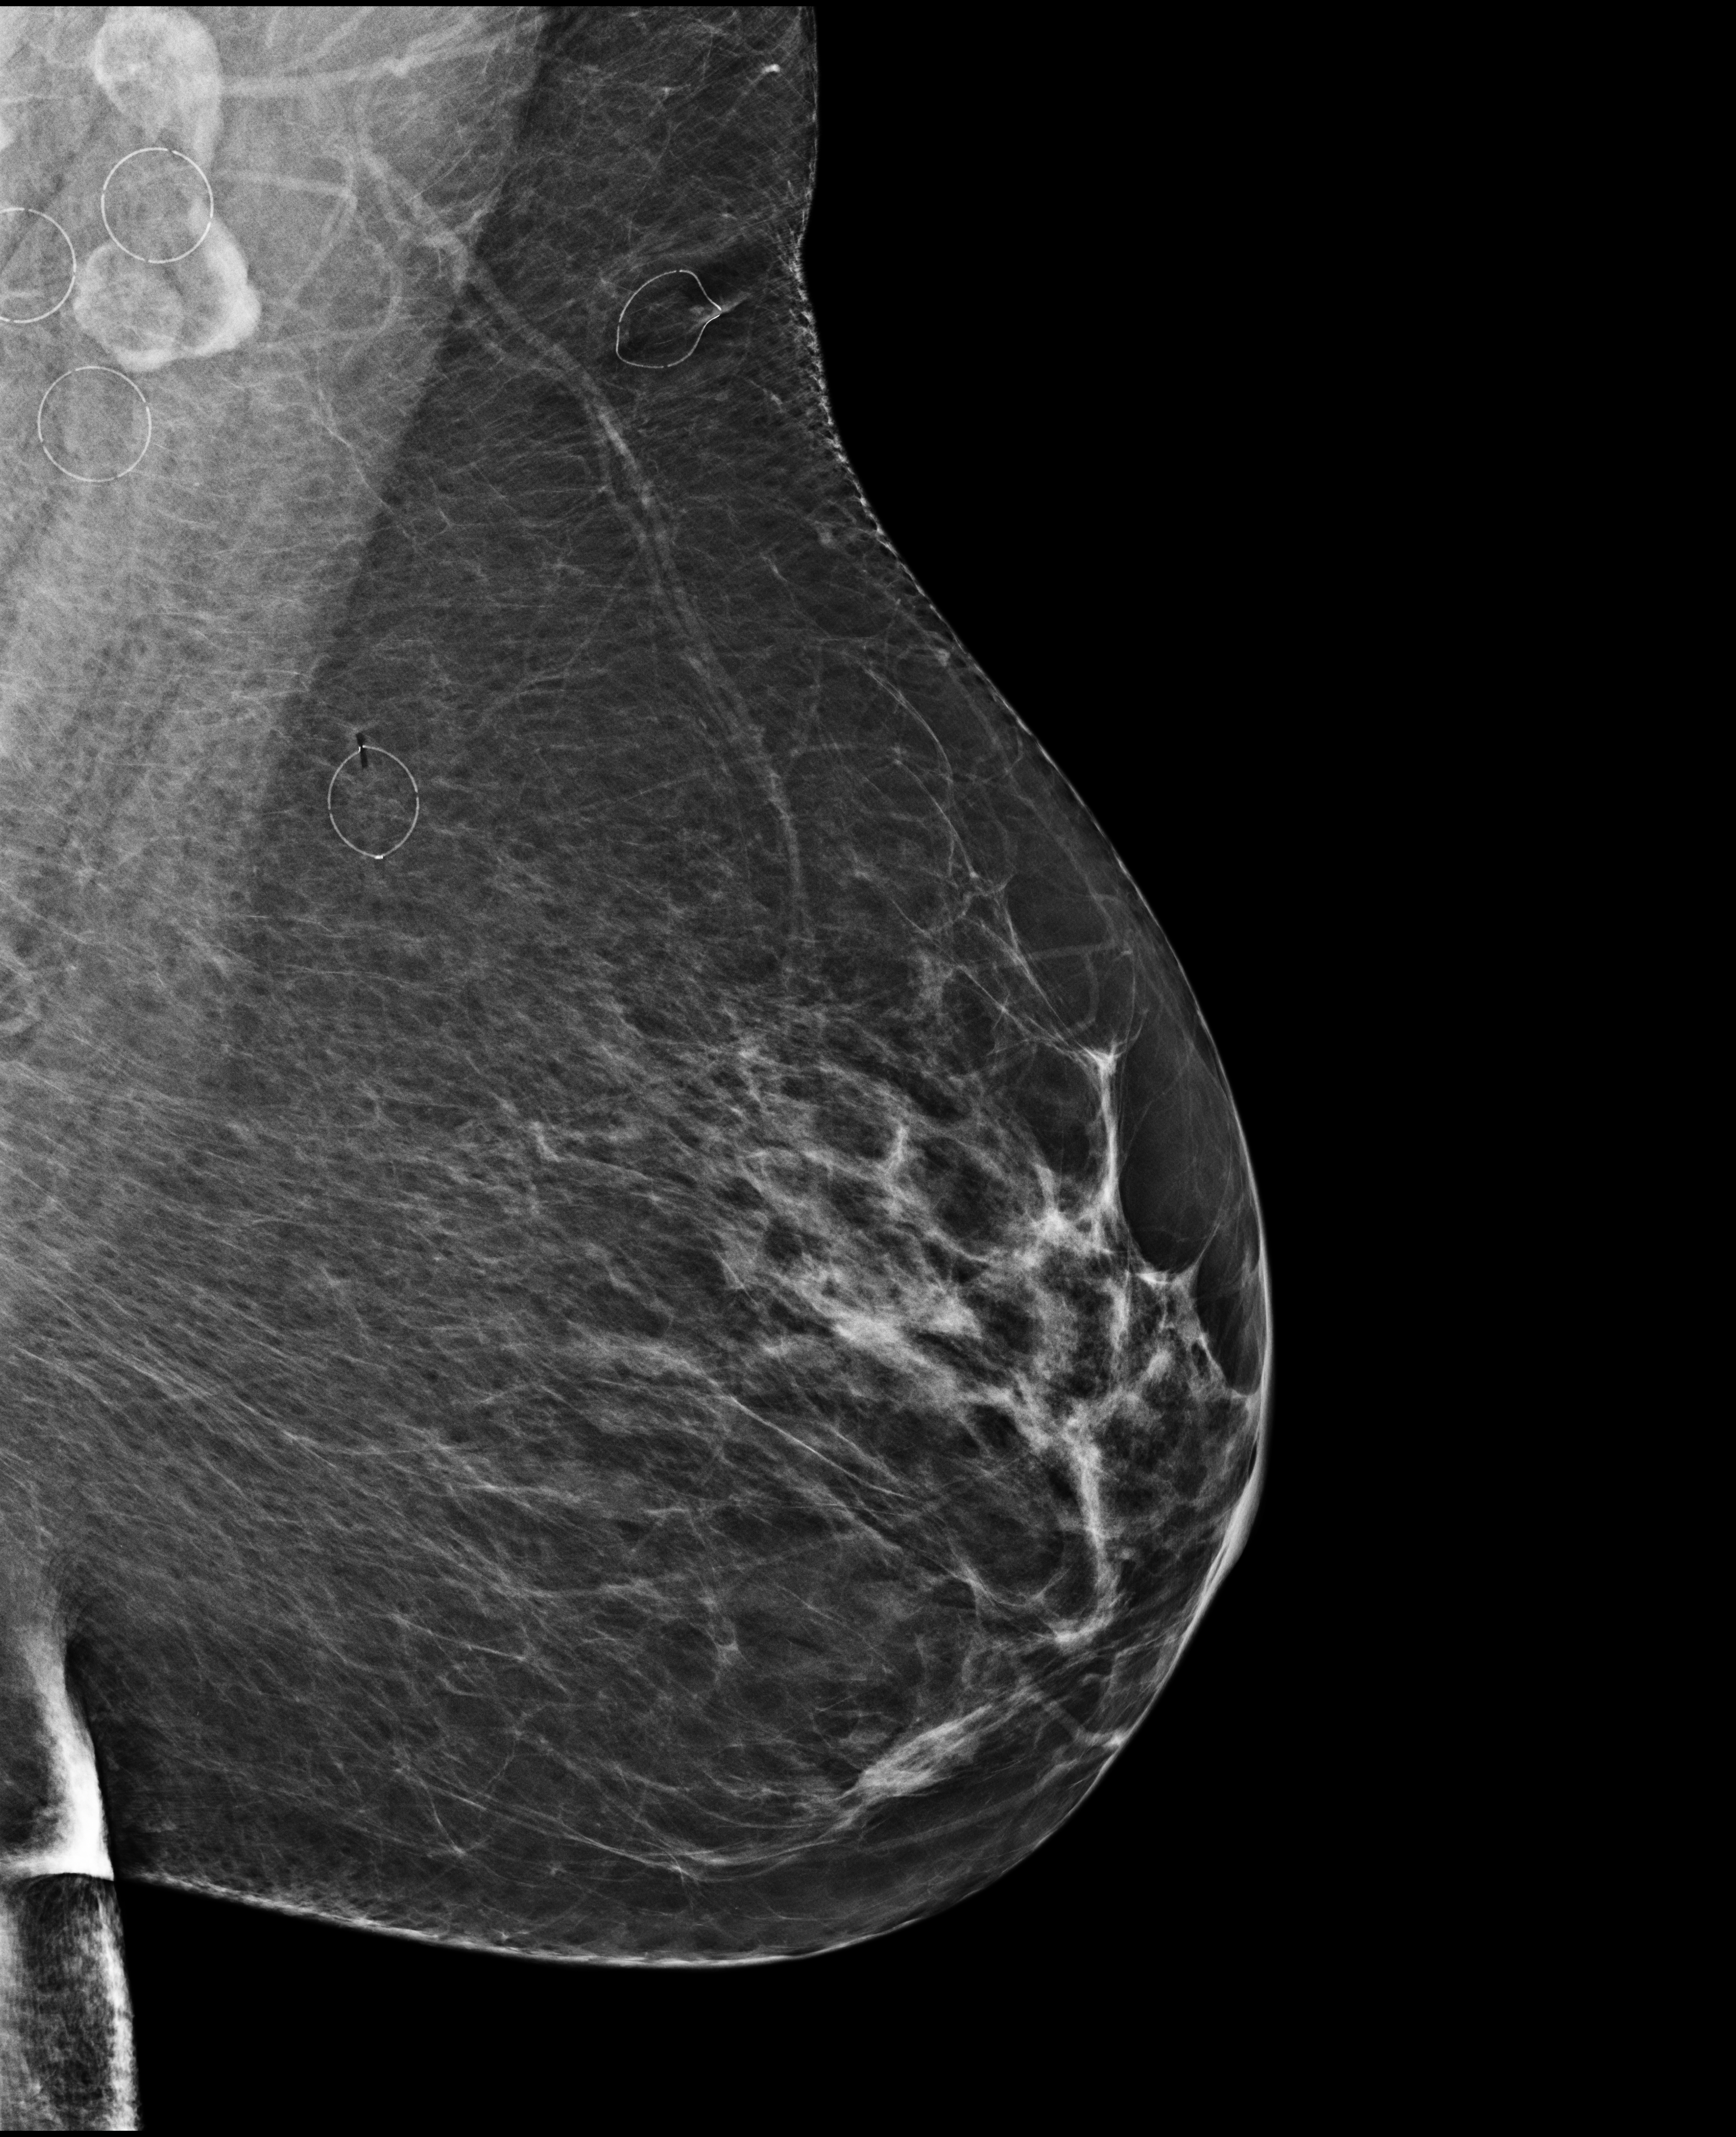
Screening examination; compressed breast thickness 70 mm. Female patient, age 67 years.
Image type: full-field digital mammogram. Breast: left. Projection: MLO view.